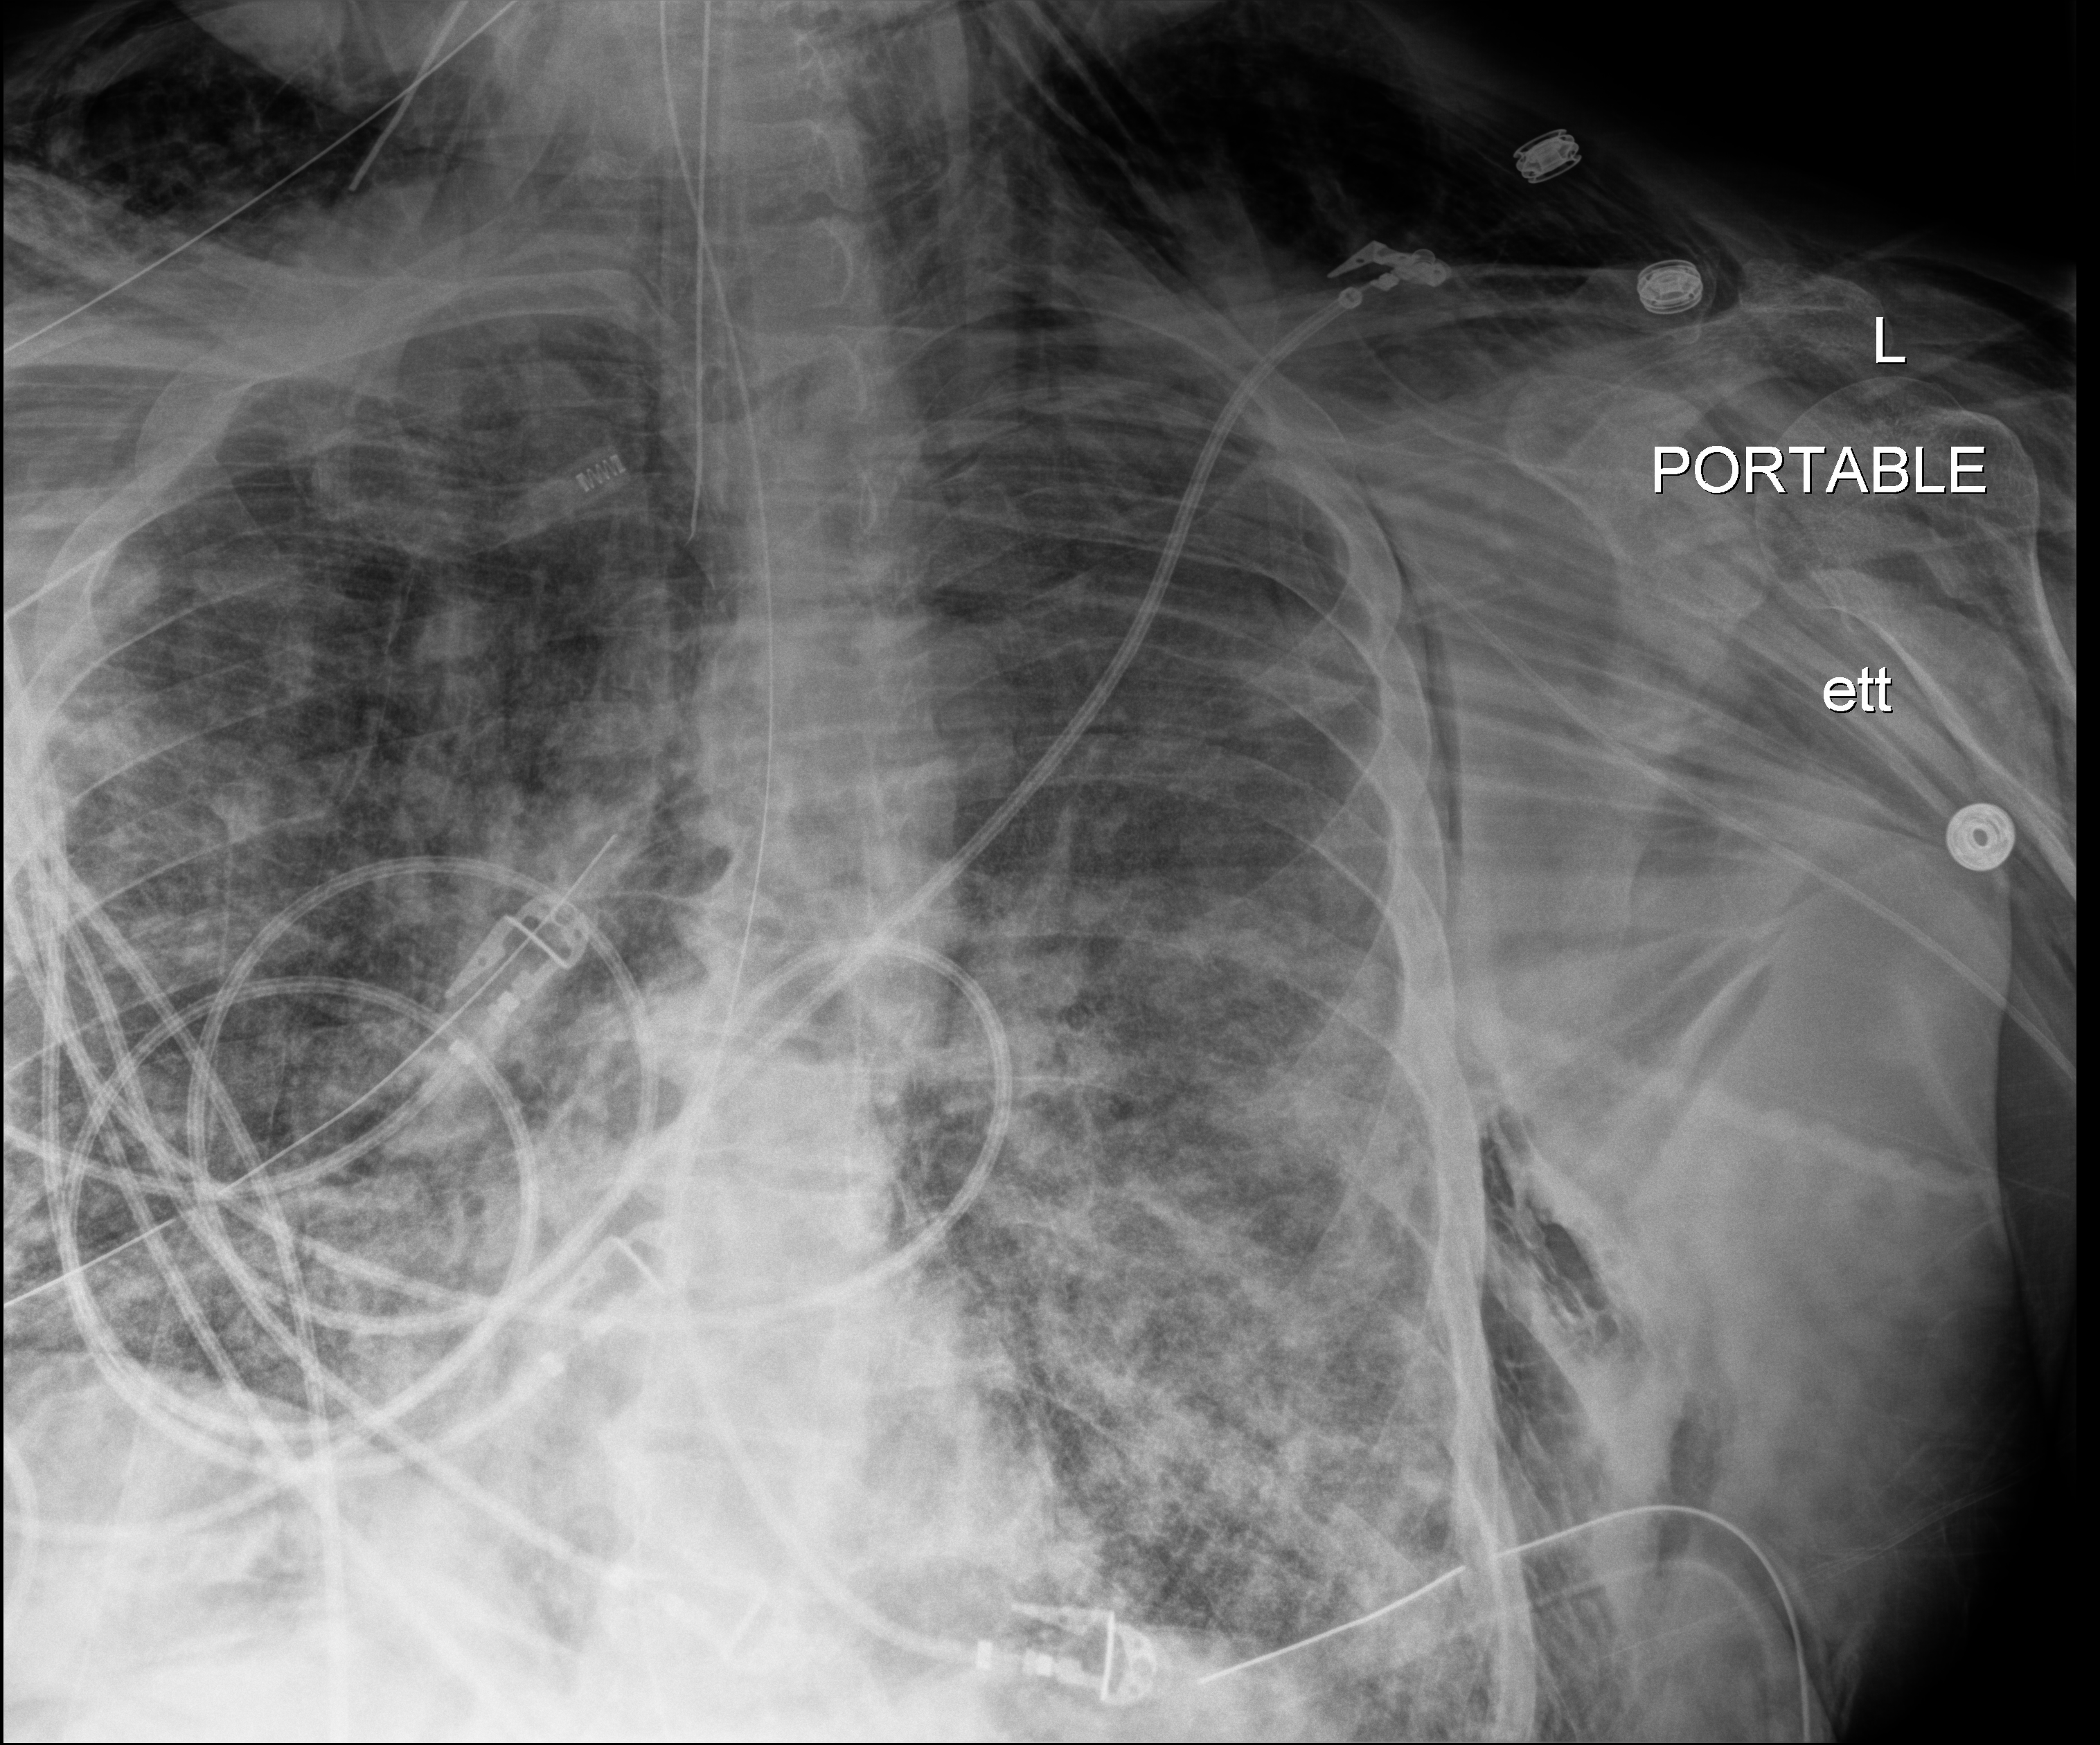
Portable chest radiograph, anteroposterior (AP) projection. Patient hospitalised with COVID-19, aged 18–59 years.
Admission-level facts for this patient (not findings on this image; timing relative to this image not recorded):
- admitted to intensive care during this hospital stay: yes
- mechanically ventilated during this hospital stay: yes
- chronic kidney disease (admission record): no